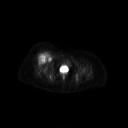
FDG PET of an extremity soft-tissue mass (from a PET/CT study), one axial slice; position 63 of 267 along the scan axis; 3.27 mm slice thickness; 128 × 128 image matrix, field of view 700 × 700 mm. Female patient, age 56 years. From the clinical record (not read from this slice): histological type: malignant solitary fibrous tumor; grade: intermediate; site of the primary tumour: right thigh.
Annotated regions visible in this slice (expert contour drawn on MRI and transferred to this co-registered scan by the dataset authors):
- gross tumour volume including surrounding oedema: bounding box (x1, y1, x2, y2) in pixels: (36, 52, 50, 62)
- gross tumour volume (mass): (40, 53, 47, 59)